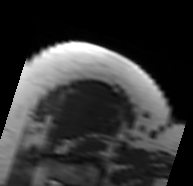
MRI of an extremity soft-tissue mass, one axial slice. Position 61 of 91 along the scan axis. MR volume resampled by the dataset authors to the PET/CT grid (not the native acquisition matrix). 3.27 mm slice thickness. 193 × 186 image matrix. Female patient. Case-level facts recorded for this patient, not image findings: histological type: malignant solitary fibrous tumor; grade: intermediate; site of the primary tumour: right thigh.
Structures marked on this image (expert contour drawn on MRI and transferred to this co-registered scan by the dataset authors):
- gross tumour volume including surrounding oedema: bounding box <44,88,121,150> (left, top, right, bottom; pixels)
- gross tumour volume (mass): <47,92,121,145>